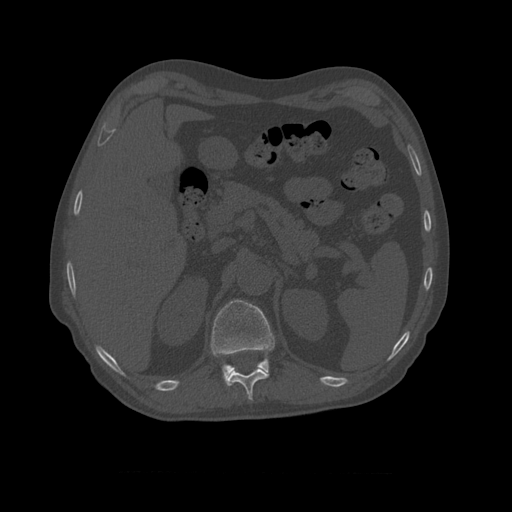
CT including the spine, one axial slice. Position 391 of 450 along the scan axis. Reconstruction kernel STANDARD. 120 kVp. Bone window (W 1800 / L 400 HU). 512 × 512 image matrix. Patient age 75 years. Case-level facts recorded for this patient, not image findings: primary cancer: prostate.
Annotated regions visible in this slice (semi-automatically segmented with operator editing):
- T10 vertebra: bounding box (x1, y1, x2, y2) in pixels: (226, 368, 270, 401)
- T11 vertebra: (211, 300, 275, 383)